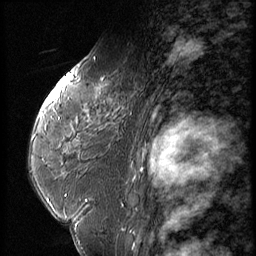
Breast MRI (dynamic contrast-enhanced), one sagittal slice; position 35 of 56 along the scan axis; dynamic contrast-enhanced series, image 2 of 3 at this slice position (ordered by acquisition); 1.5 T; TE 4.2 ms, TR 9 ms; 2.5 mm slice thickness; 256 × 256 image matrix, field of view 180 × 180 mm. Patient: female, 59 years. Case-level facts recorded for this patient, not image findings: setting: breast cancer imaged before/during neoadjuvant chemotherapy; receptor status: HER2-positive.
Structures marked on this image (semi-automatic segmentation, software-assisted and operator-edited):
- analysis volume of interest (the breast-tissue region the enhancement analysis was run in; not a lesion): bounding box (x1, y1, x2, y2) in pixels: (44, 66, 151, 135)
- tumour enhancement mask (voxels above the 140 % enhancement threshold inside the analysis volume of interest): (44, 73, 75, 106)